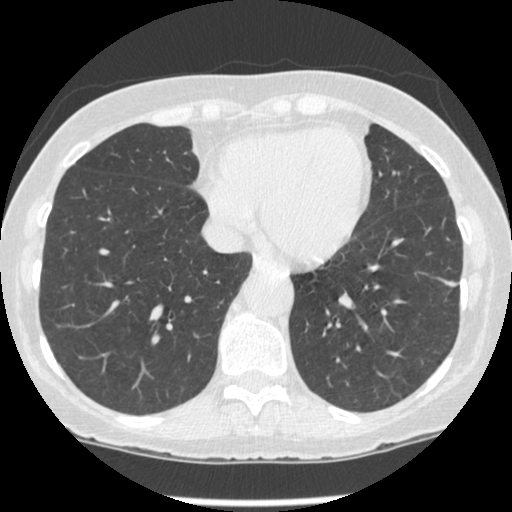
Low-dose screening chest CT, one axial slice; slice 78 of 247 in the series (ordered by position); reconstruction kernel STANDARD; lung window (W 1500 / L -600 HU); 1.25 mm slice thickness; 512 × 512 image matrix, field of view 303 × 303 mm.
Outlined on this slice (manually delineated by an expert):
- lesion 1 (tumor, lower lobe of left lung): bounding box [x1, y1, x2, y2] px = [444, 281, 457, 287]